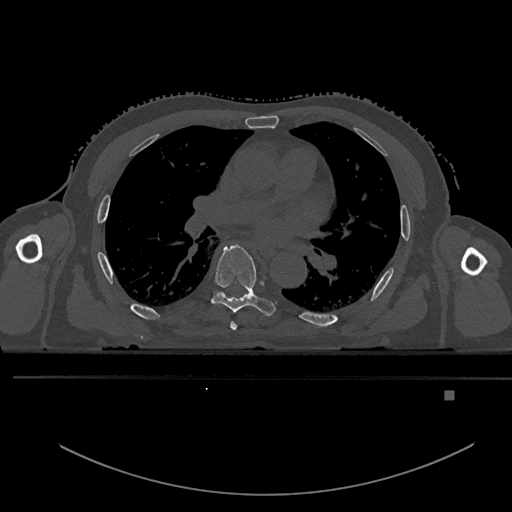
CT including the spine, one axial slice; position 308 of 969 along the scan axis; bone window (W 1800 / L 400 HU); 512 × 512 image matrix. Patient: male, 82 years. Case-level facts recorded for this patient, not image findings: primary cancer: prostate; vertebrae with lytic lesions (as recorded): T11, T9, T8, T2.
Annotated regions visible in this slice (semi-automatically segmented with operator editing):
- T5 vertebra: bounding box [x1, y1, x2, y2] px = [230, 321, 237, 331]
- T6 vertebra: [201, 245, 276, 316]